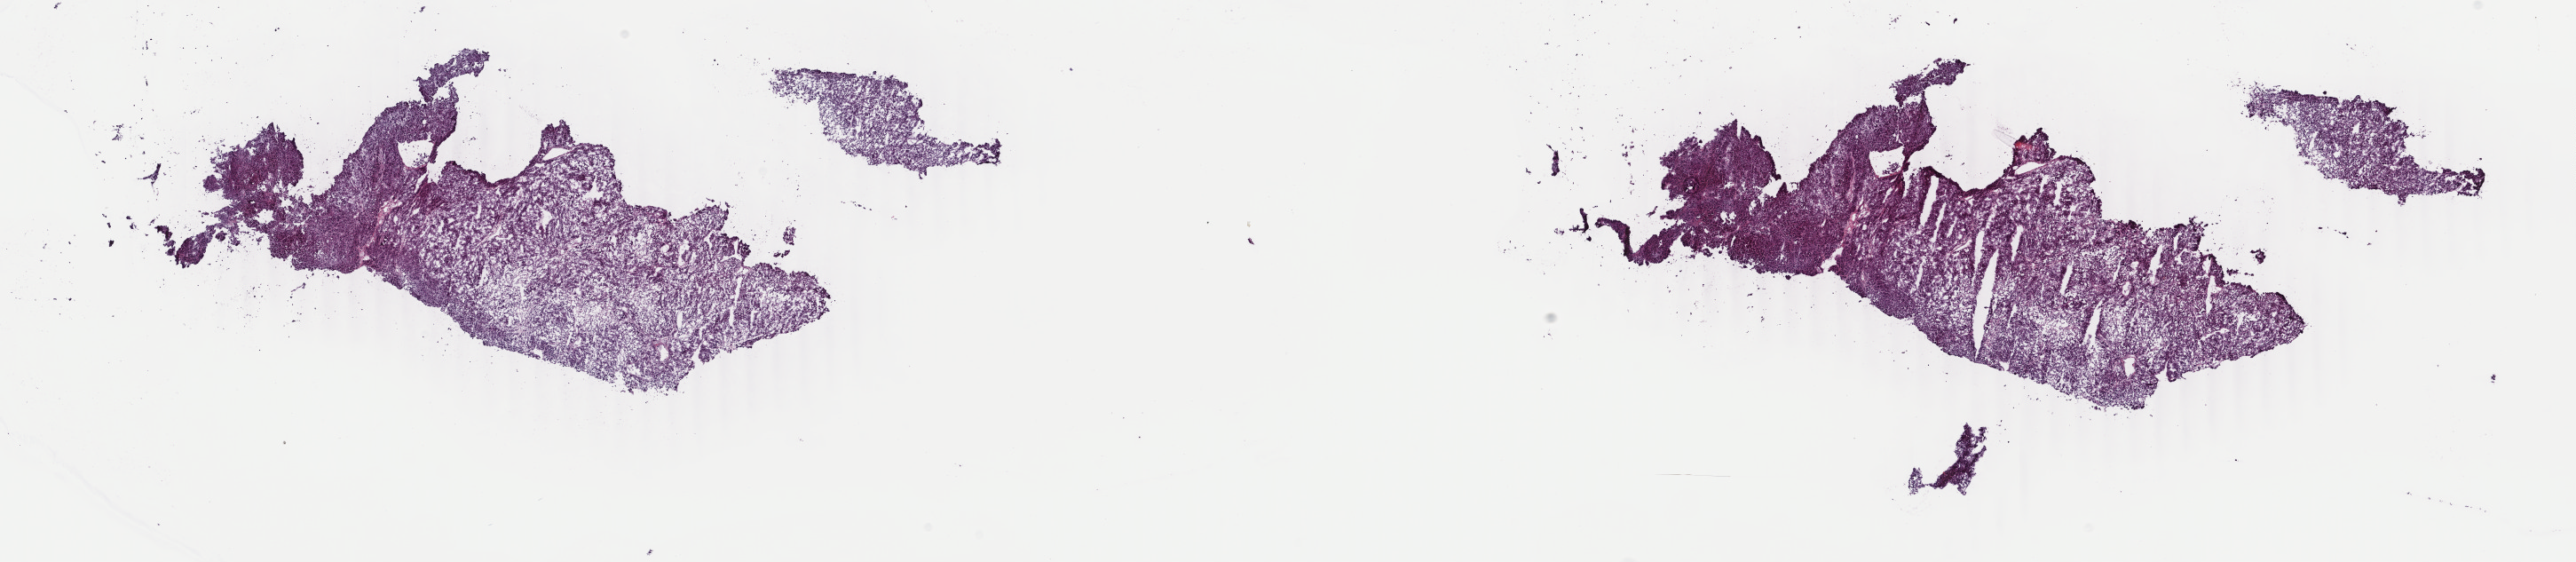
Whole-slide histology image, H&E-stained — whole scanned area (about 23.1 x 5.0 mm) shown as a low-resolution overview, frozen section from the top of the tissue portion, sample: primary tumour, adrenal cortex. Patient: male, age at initial diagnosis 46 years. Pathologist review of this section (percent, as recorded): tumour cells 95%, tumour nuclei 95%, normal cells 0%, stromal cells 0%, necrosis 5%. Inflammatory infiltration, as recorded: lymphocyte infiltration 20%, monocyte infiltration 20%, neutrophil infiltration 40%.
- histologic diagnosis: Adrenal cortical carcinoma (cortex of adrenal gland)
- lymph nodes positive (case pathology): 0 of 1 examined